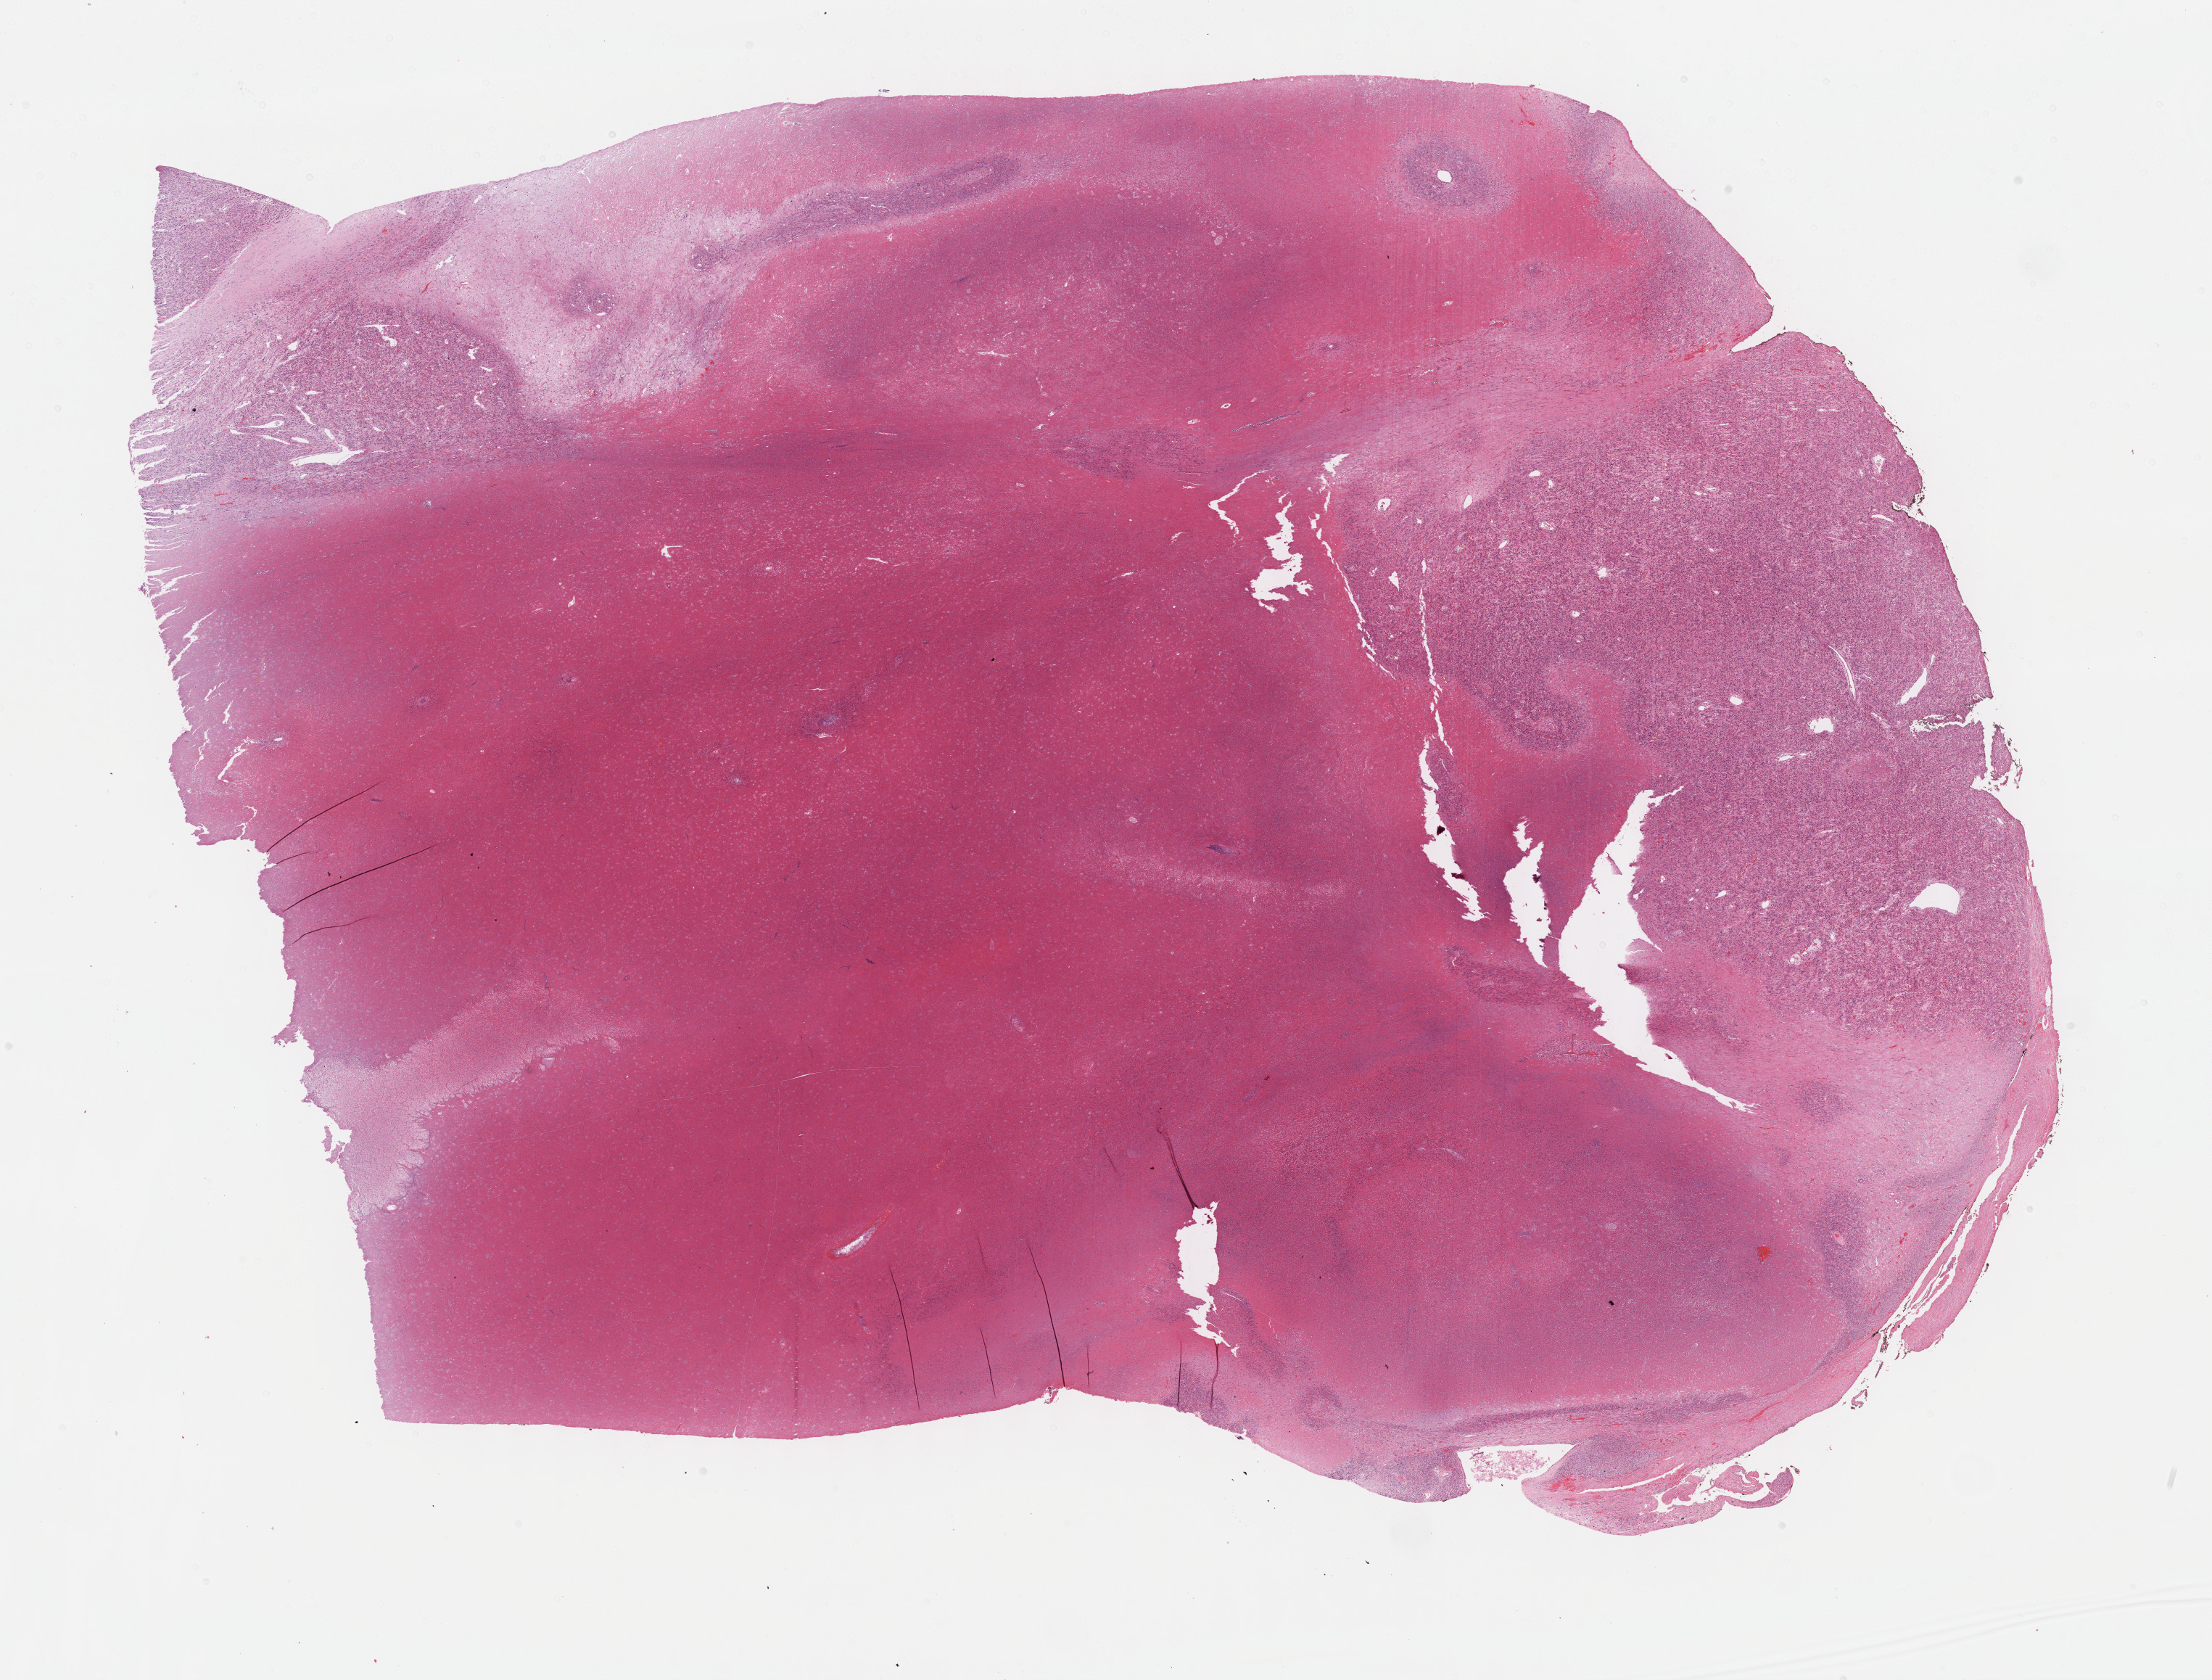
Whole-slide histology image, H&E, a low-resolution overview of the entire scanned area, about 24.7 x 18.7 mm (from a 40x scan); formalin-fixed paraffin-embedded (FFPE) diagnostic section; retroperitoneum and peritoneum, primary tumour sample. Patient: female, age at initial diagnosis 53 years.
* diagnosis: Leiomyosarcoma, NOS (retroperitoneum)